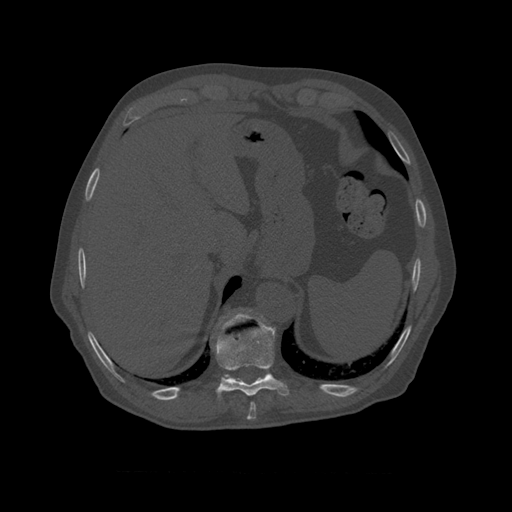
CT including the spine, one axial slice; position 421 of 450 along the scan axis; reconstruction kernel STANDARD; 120 kVp; bone window (W 1800 / L 400 HU); 1.25 mm slice thickness; 512 × 512 image matrix, field of view 405 × 405 mm. Patient age 75 years. From the clinical record (not read from this slice): primary cancer: prostate.
Annotated regions visible in this slice (semi-automatic segmentation, software-assisted and operator-edited):
- T10 vertebra: bounding box (x1, y1, x2, y2) in pixels: (218, 309, 272, 378)
- T8 vertebra: (250, 402, 256, 411)
- T9 vertebra: (215, 321, 290, 397)